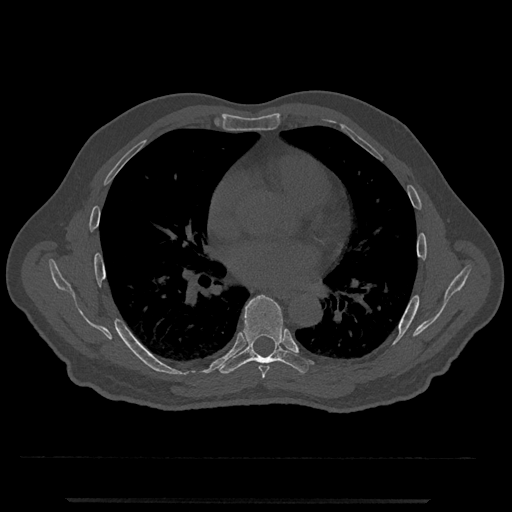
CT including the spine, one axial slice; slice 700 of 797 in the series (ordered by position); reconstruction kernel Br40s/3; 120 kVp; bone window (W 1800 / L 400 HU); 0.5 mm slice thickness; 512 × 512 image matrix. Male patient, age 63 years. Case-level facts recorded for this patient, not image findings: primary cancer: prostate.
Outlined on this slice (semi-automatic segmentation, software-assisted and operator-edited):
- T6 vertebra: box from (x=259, y=366) to (x=270, y=379) px
- T7 vertebra: (x=217, y=295)–(x=313, y=374)